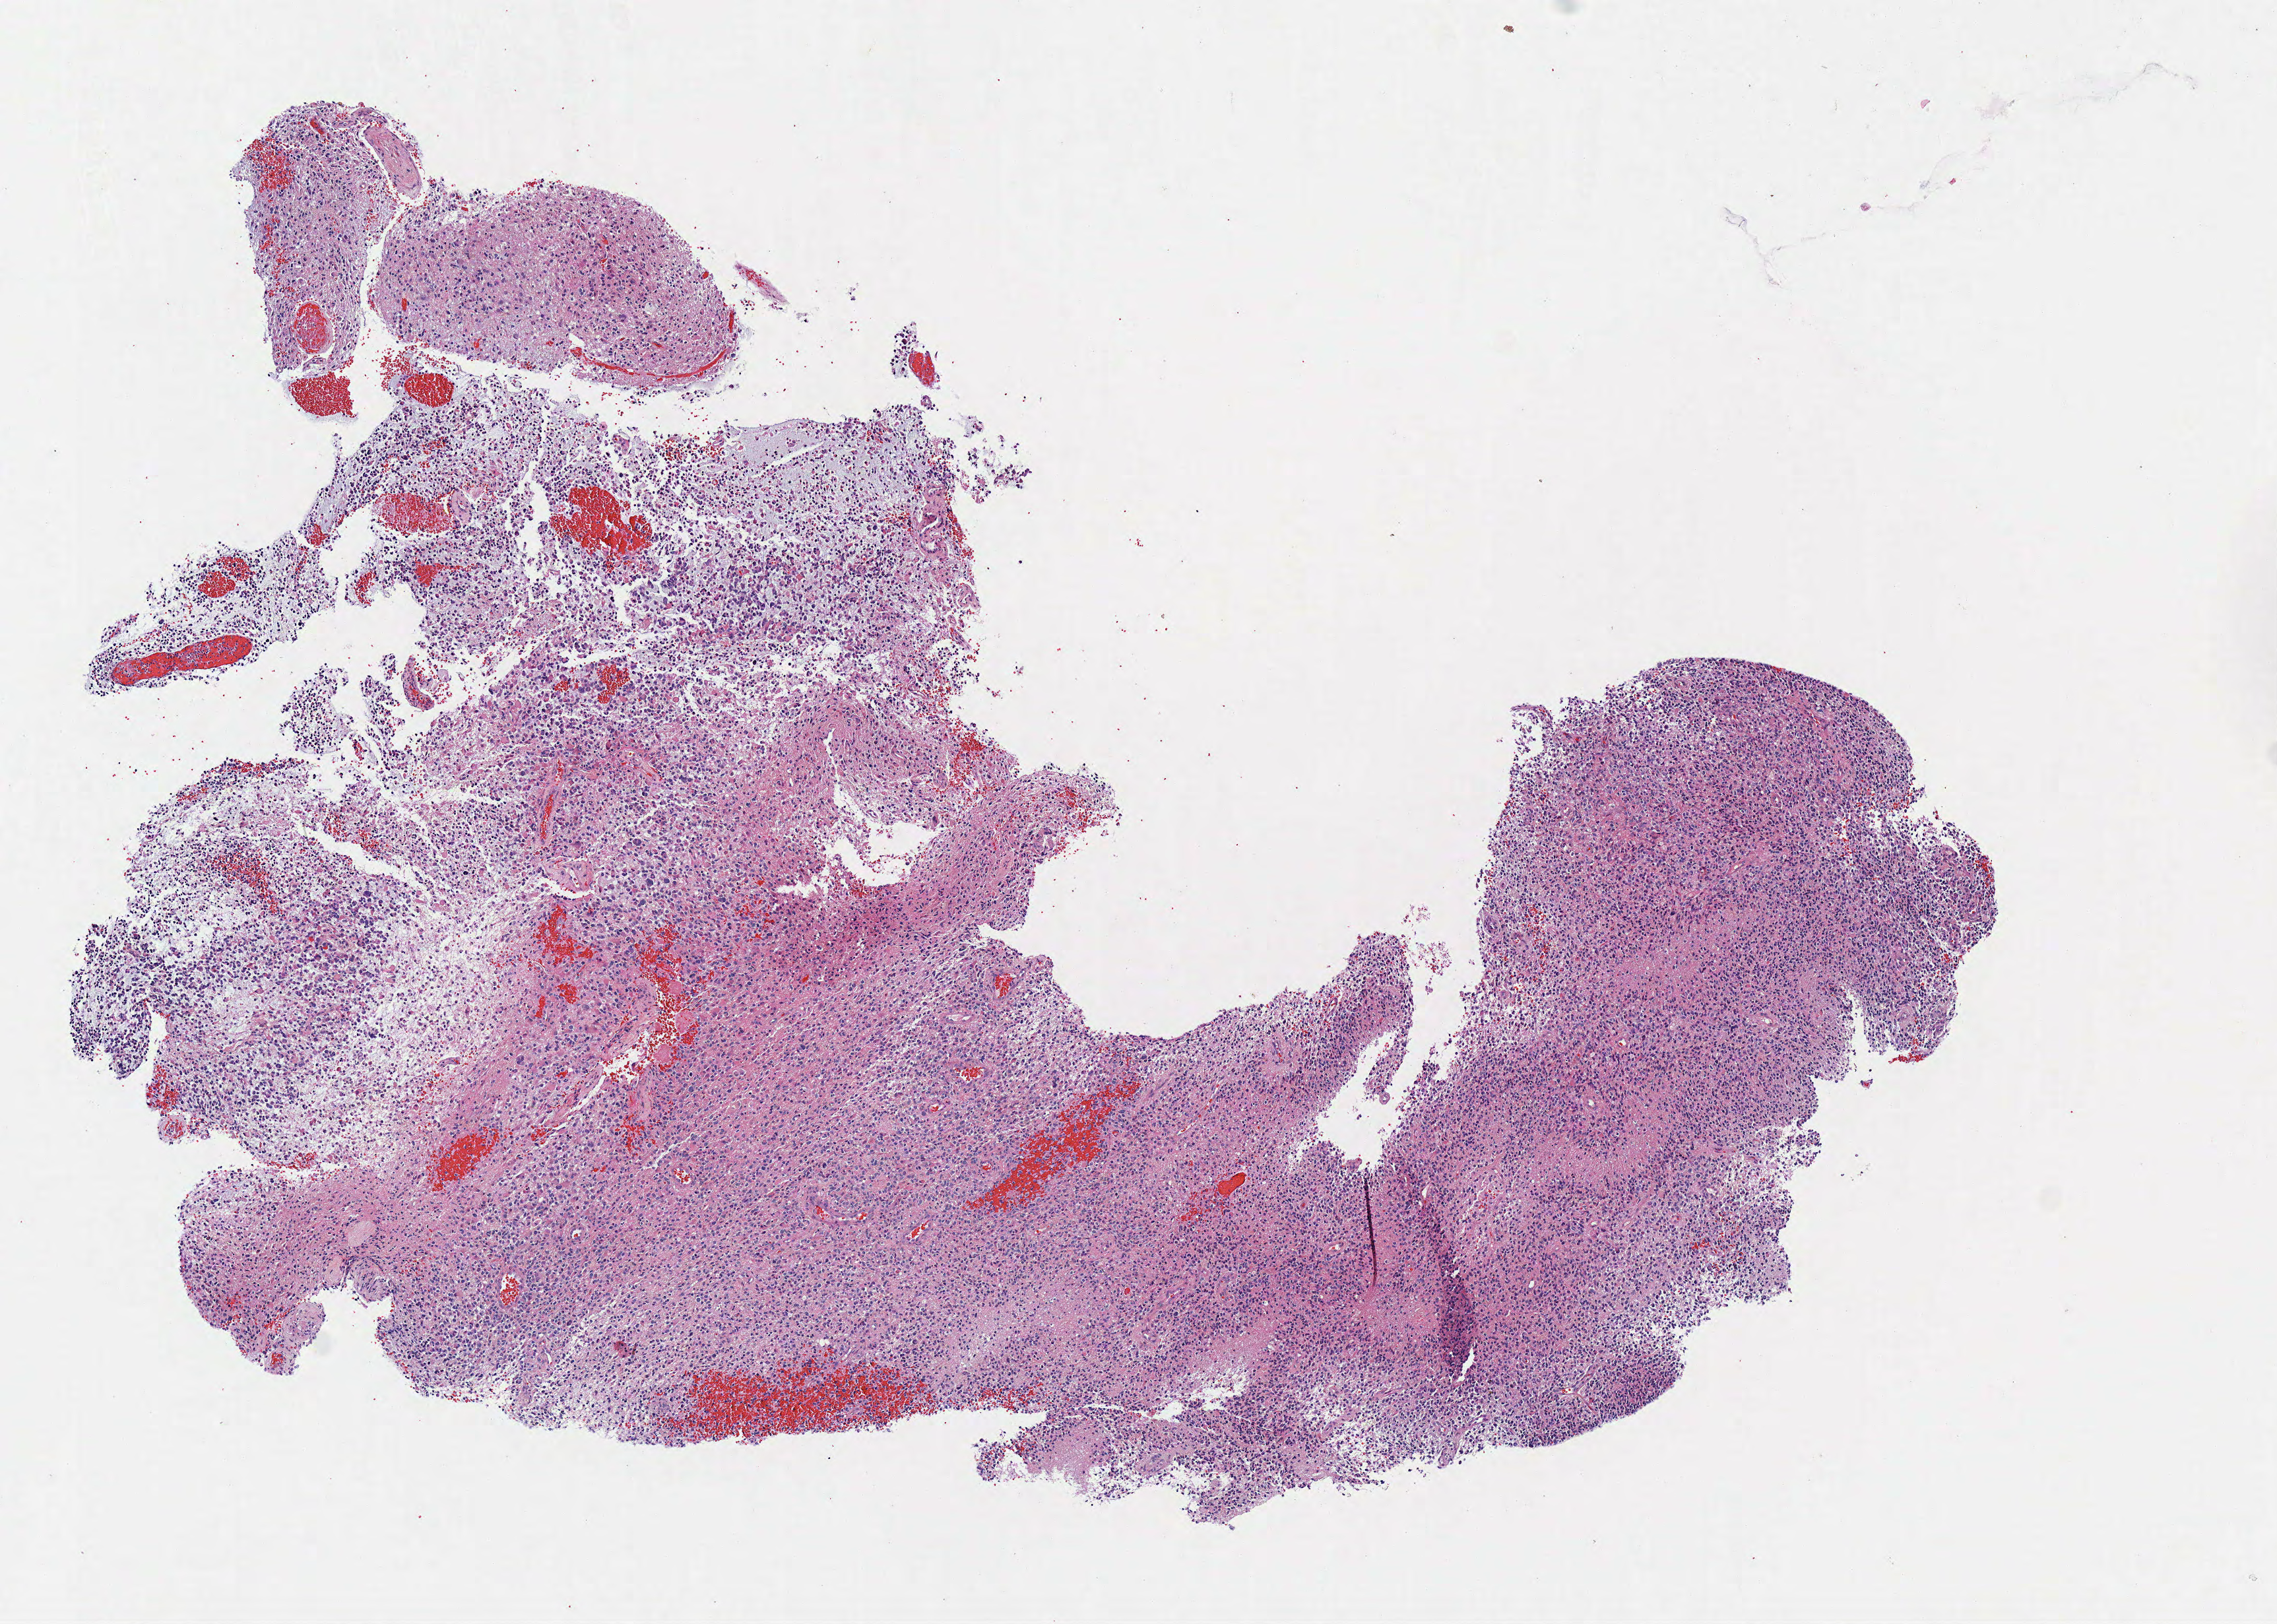
H&E whole-slide image, a low-resolution overview of the entire scanned area, about 6.8 x 4.8 mm; frozen section; primary tumour sample from the brain. Patient: male, age at initial diagnosis 58 years. Composition of this section per pathologist review: tumour cells 95%, tumour nuclei 85%, normal cells 0%, stromal cells 0%, necrosis 5%.
Pathologic diagnosis: Glioblastoma.